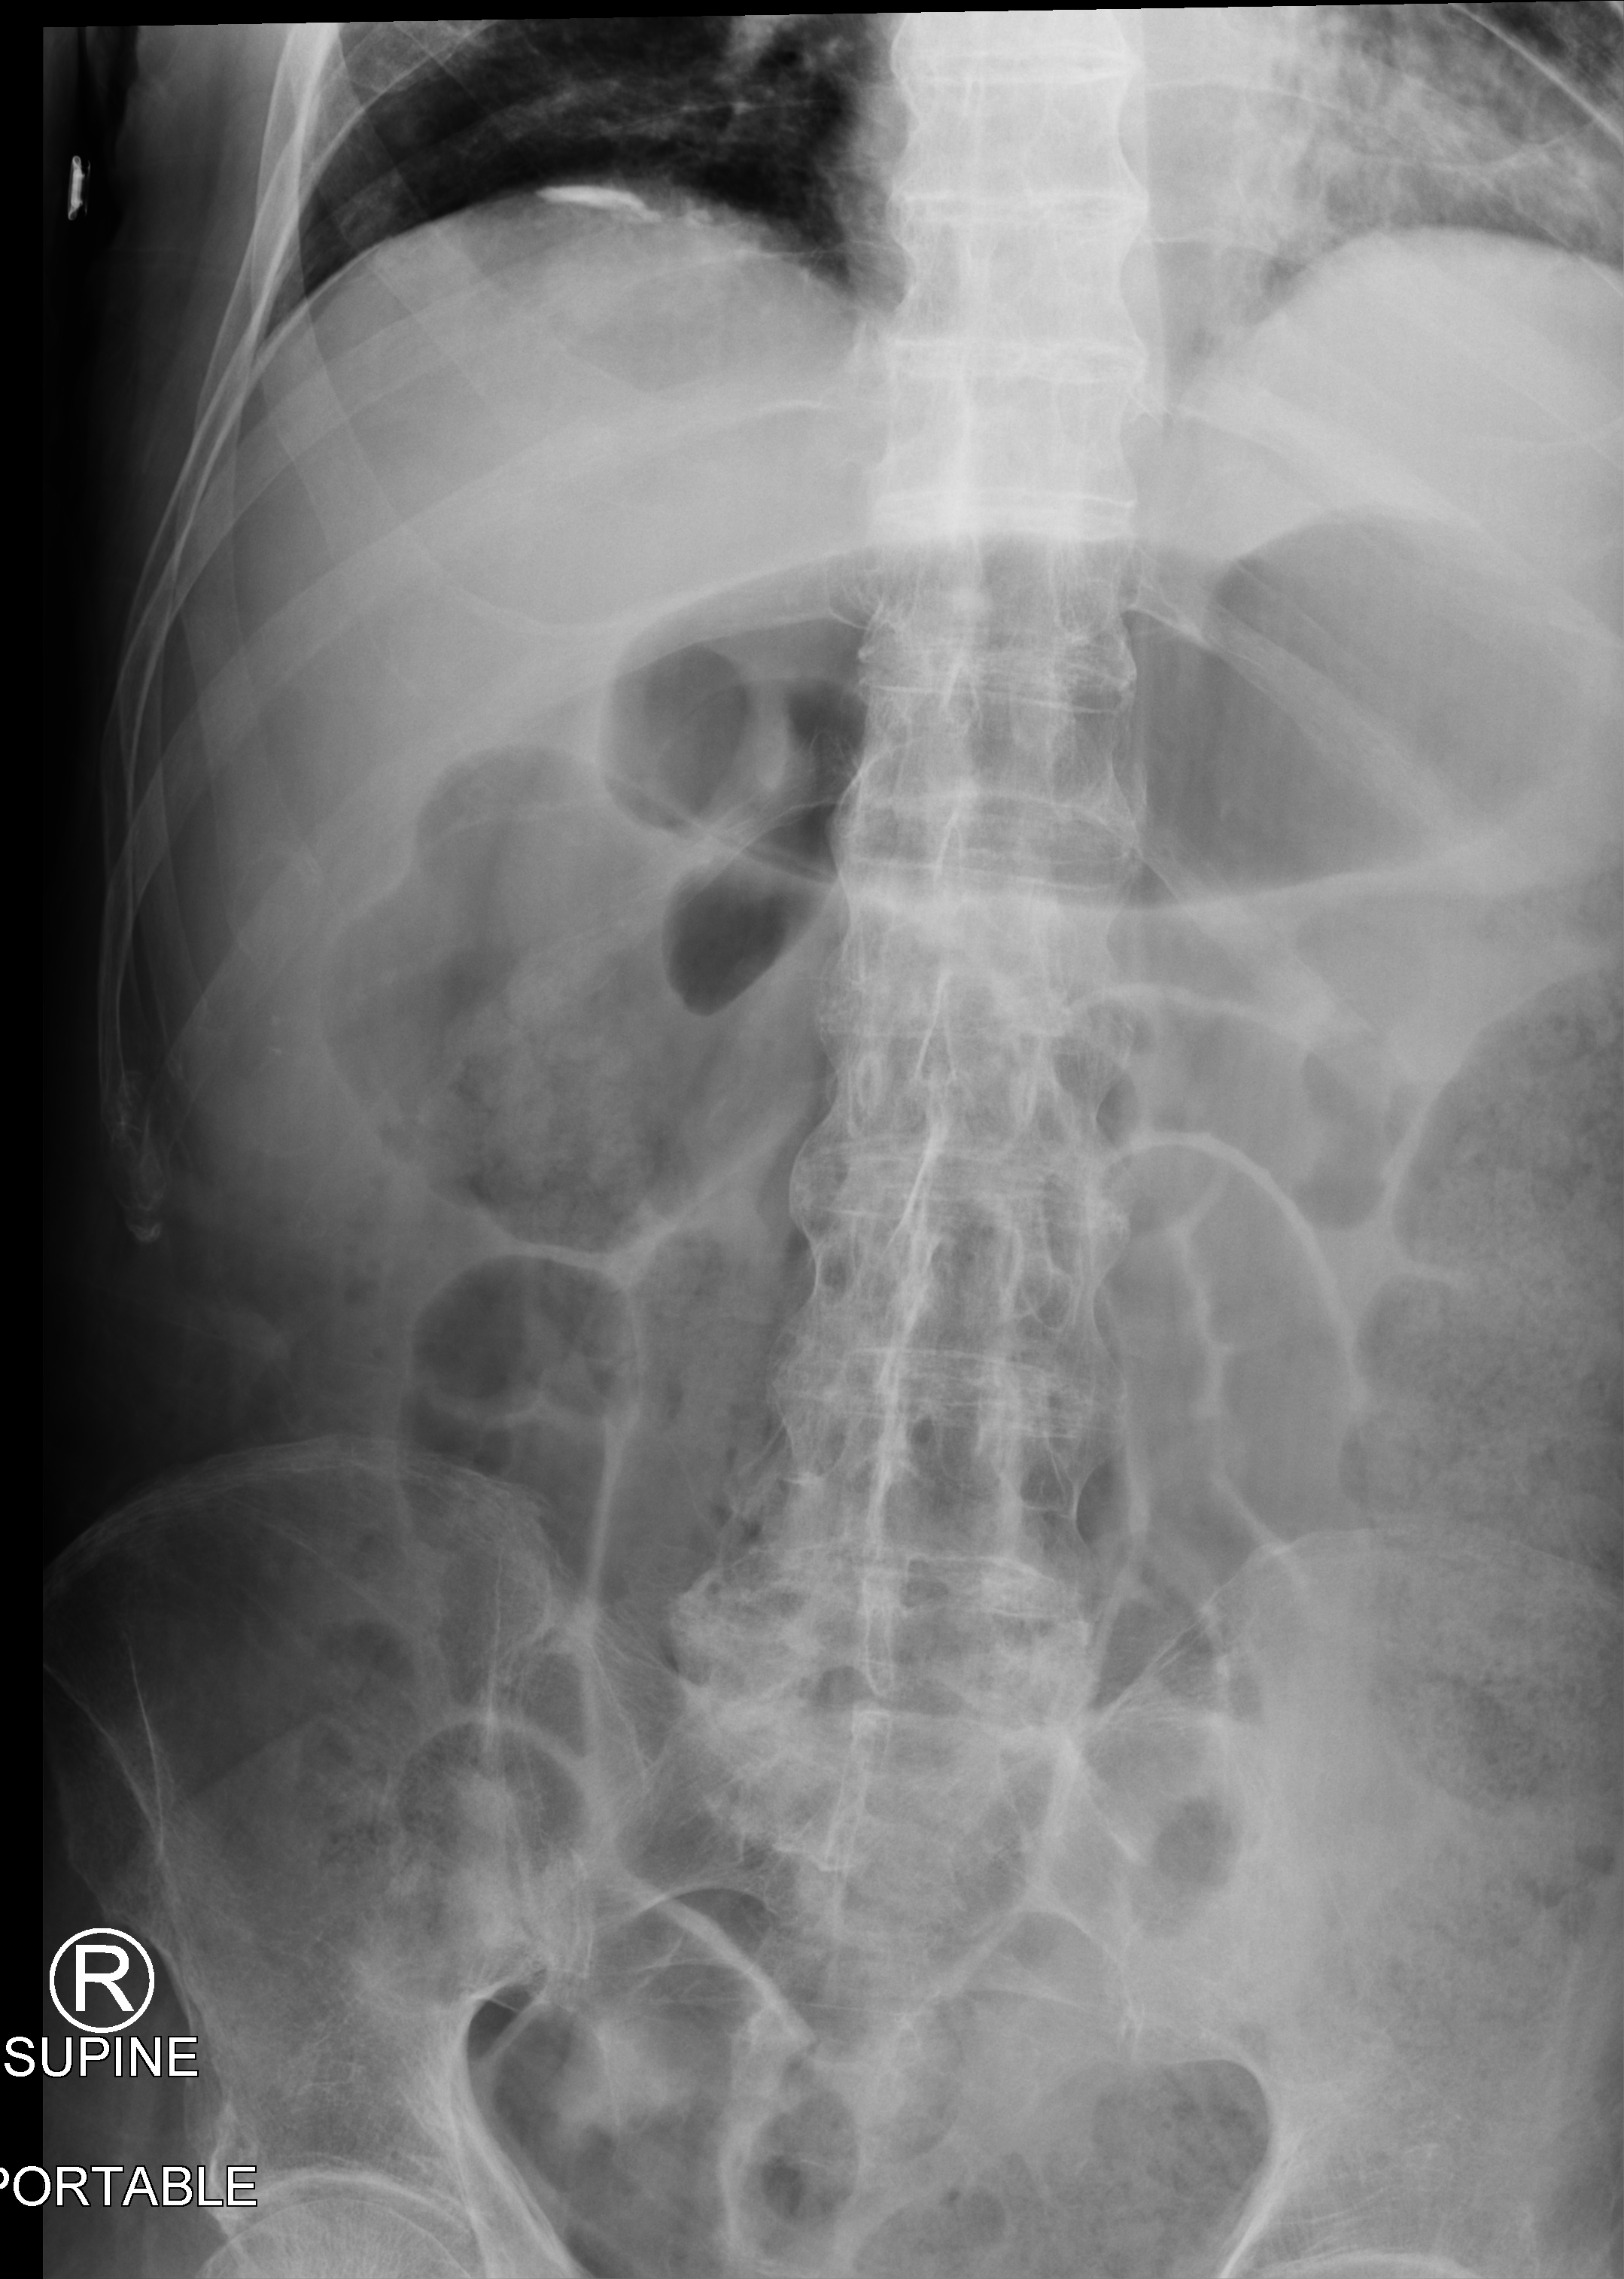
Portable abdomen radiograph; anteroposterior (AP) projection. Patient hospitalised with COVID-19; male, aged 75–90 years.
Admission-level facts for this patient (not findings on this image; timing relative to this image not recorded):
- admitted to intensive care during this hospital stay: no
- length of hospital stay: 1 day
- mechanically ventilated during this hospital stay: no